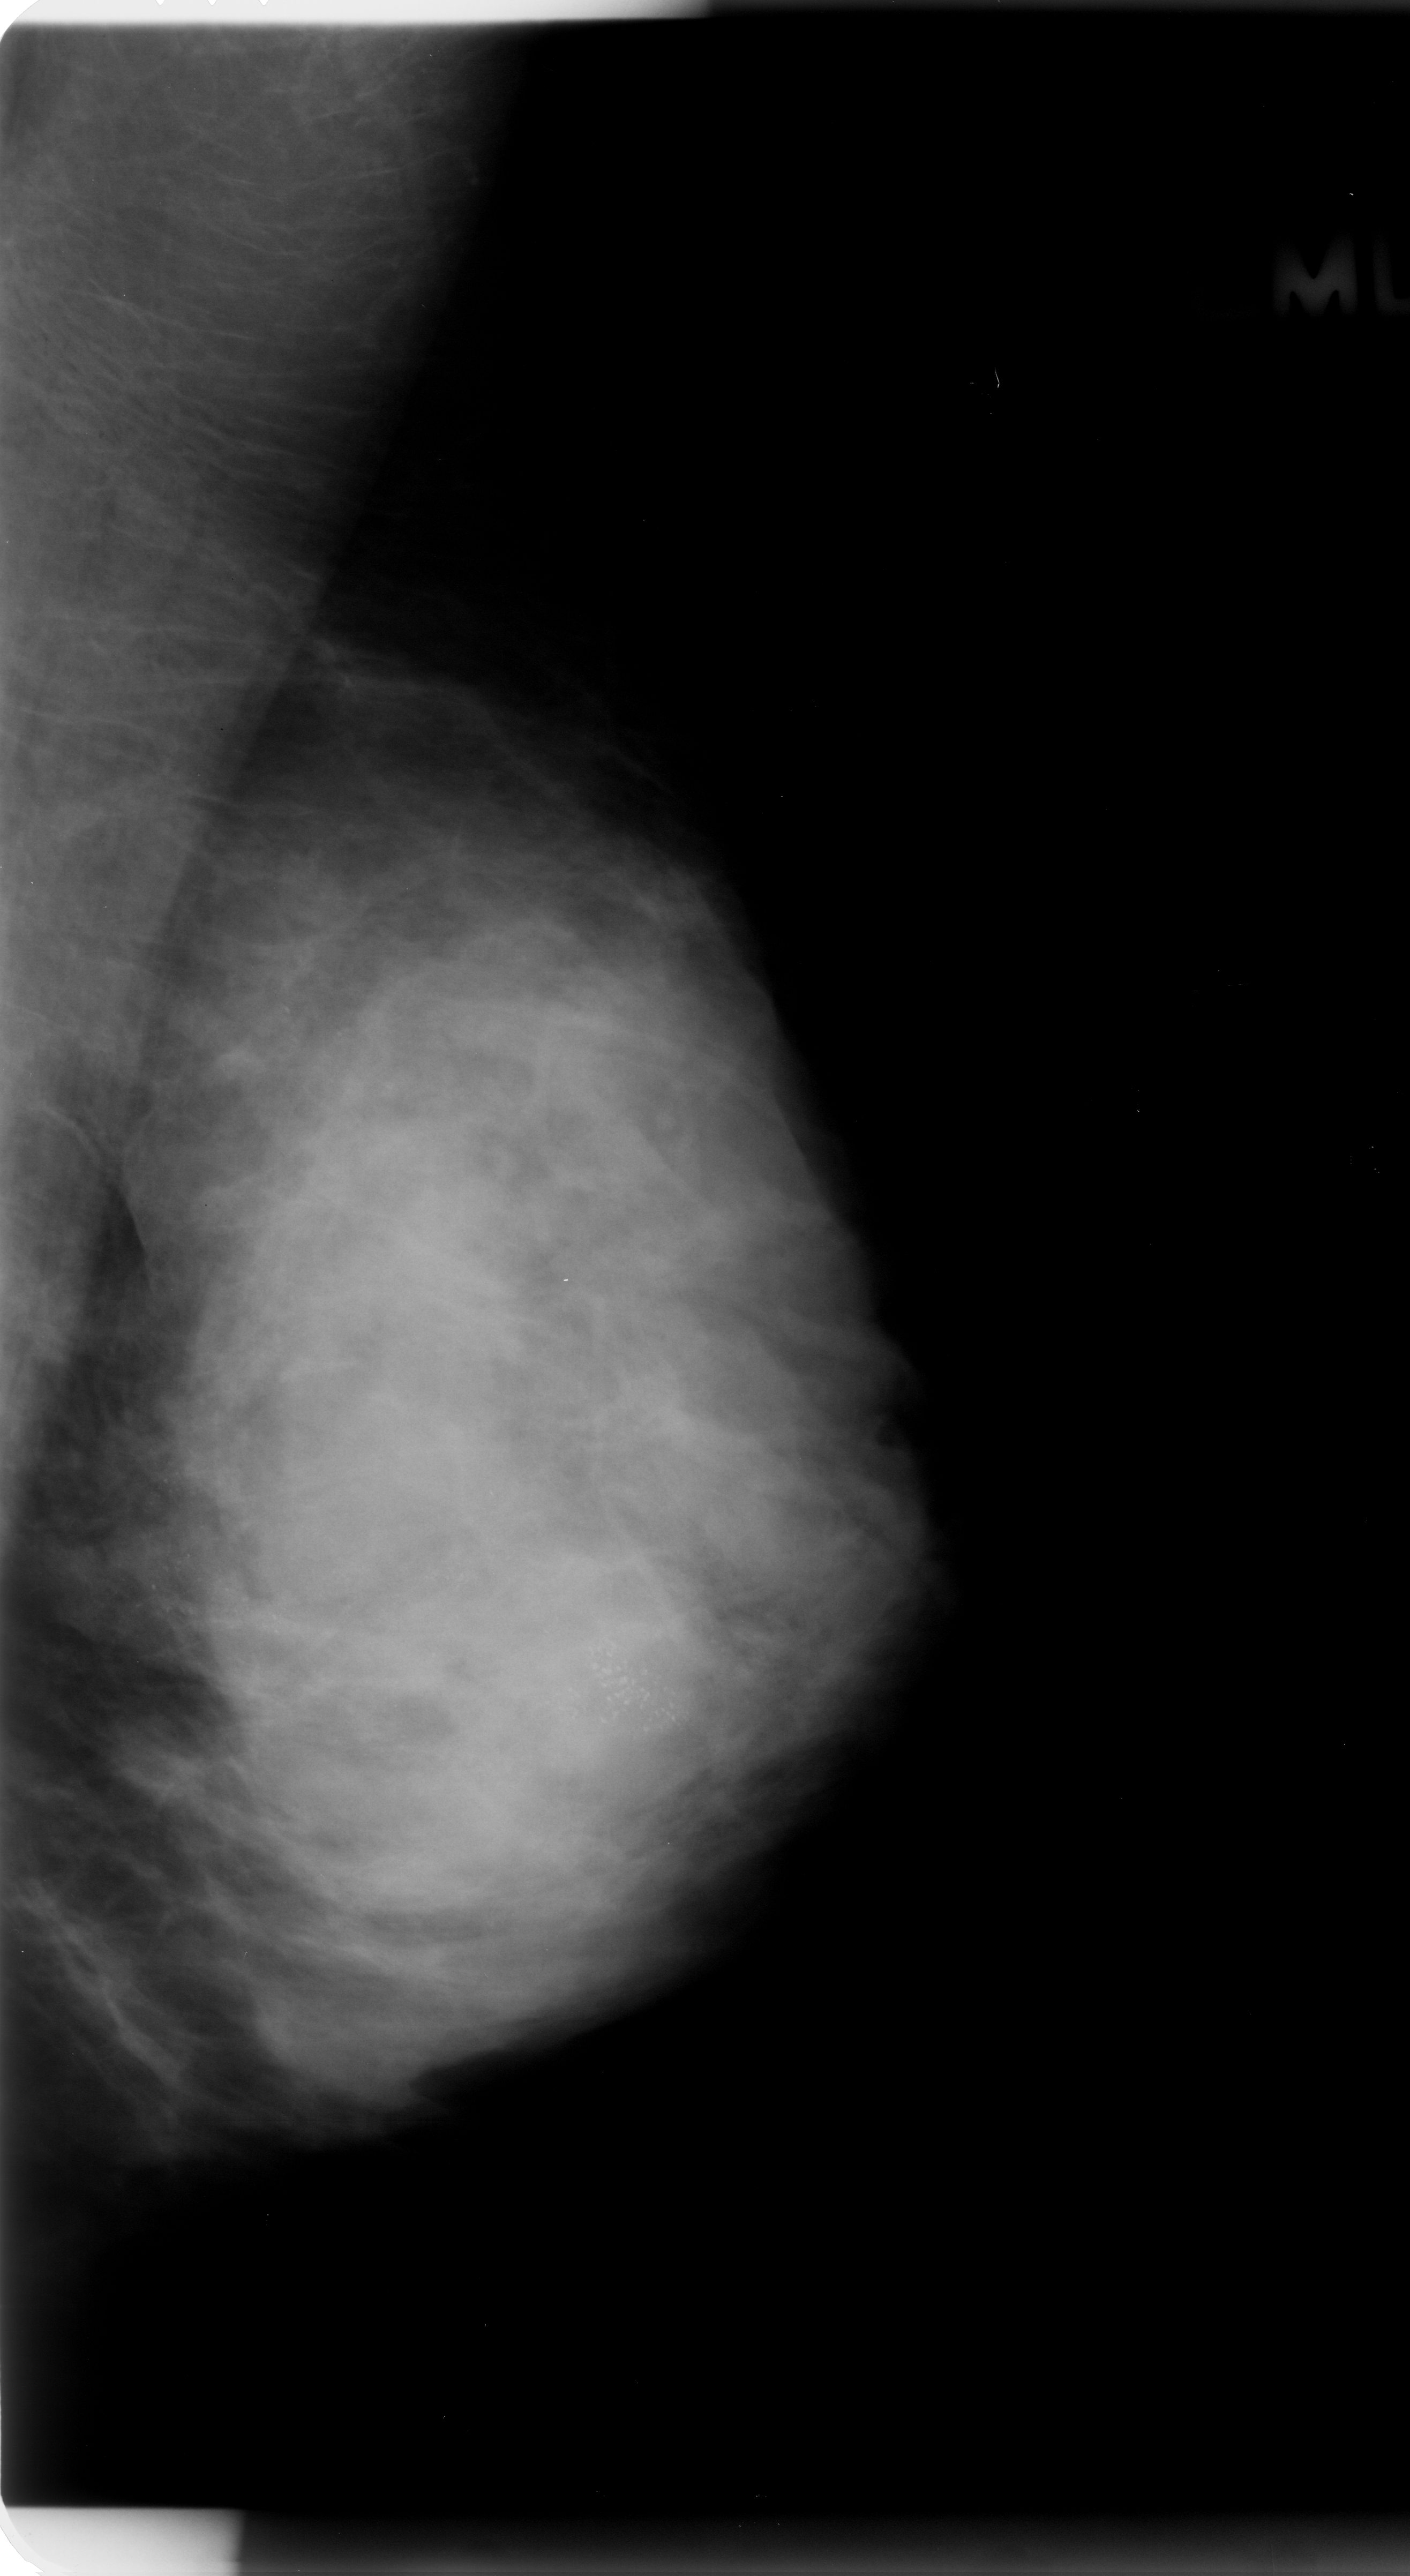
Digitized screen-film mammogram; left breast; MLO view; BI-RADS breast density category 4 (scale 1–4).
Marked findings (only marked abnormalities are described; nothing is implied about the rest of the image): calcifications, morphology amorphous / pleomorphic, distribution segmental; BI-RADS assessment category 5; subtlety rating 5 on a 1 (subtle) to 5 (obvious) scale; pathology result (as recorded, not read from the image): malignant.